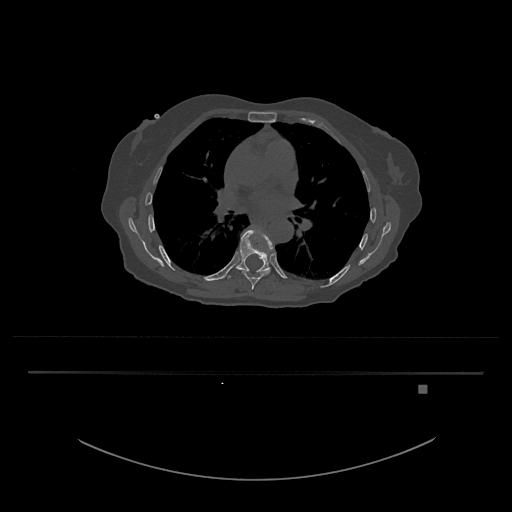
CT including the spine, one axial slice; slice 782 of 797 in the series (ordered by position); reconstruction kernel Br40s/3; 120 kVp; bone window (W 1800 / L 400 HU); 0.5 mm slice thickness; 512 × 512 image matrix. Female patient, age 57 years. From the clinical record (not read from this slice): primary cancer: cervical.
Annotated regions visible in this slice (semi-automatic segmentation, software-assisted and operator-edited):
- T8 vertebra: bounding box <242,233,273,290> (left, top, right, bottom; pixels)
- T9 vertebra: <225,228,274,279>